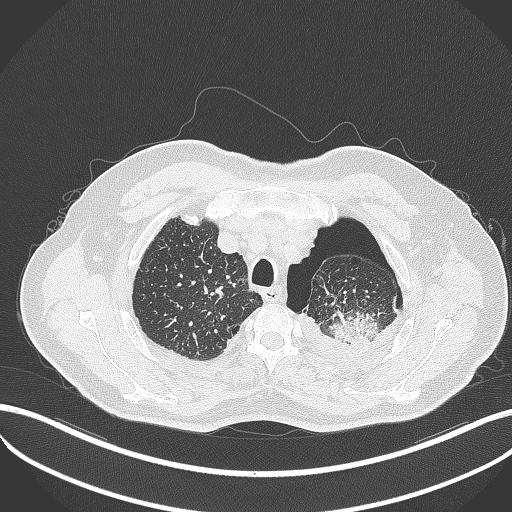
Chest CT, one axial slice. Slice 417 of 464 in the series (ordered by position). Reconstruction kernel B70f. 120 kVp. Lung window (W 1500 / L -600 HU). 1 mm slice thickness. 512 × 512 image matrix, field of view 400 × 400 mm. Patient: male, 76 years. Case-level facts recorded for this patient, not image findings: clinical TNM (as recorded): T3 N0 M1b.
Structures marked on this image (rectangle marked by the reading radiologist):
- lung tumour (recorded histology: adenocarcinoma): box from (x=326, y=307) to (x=385, y=348) px